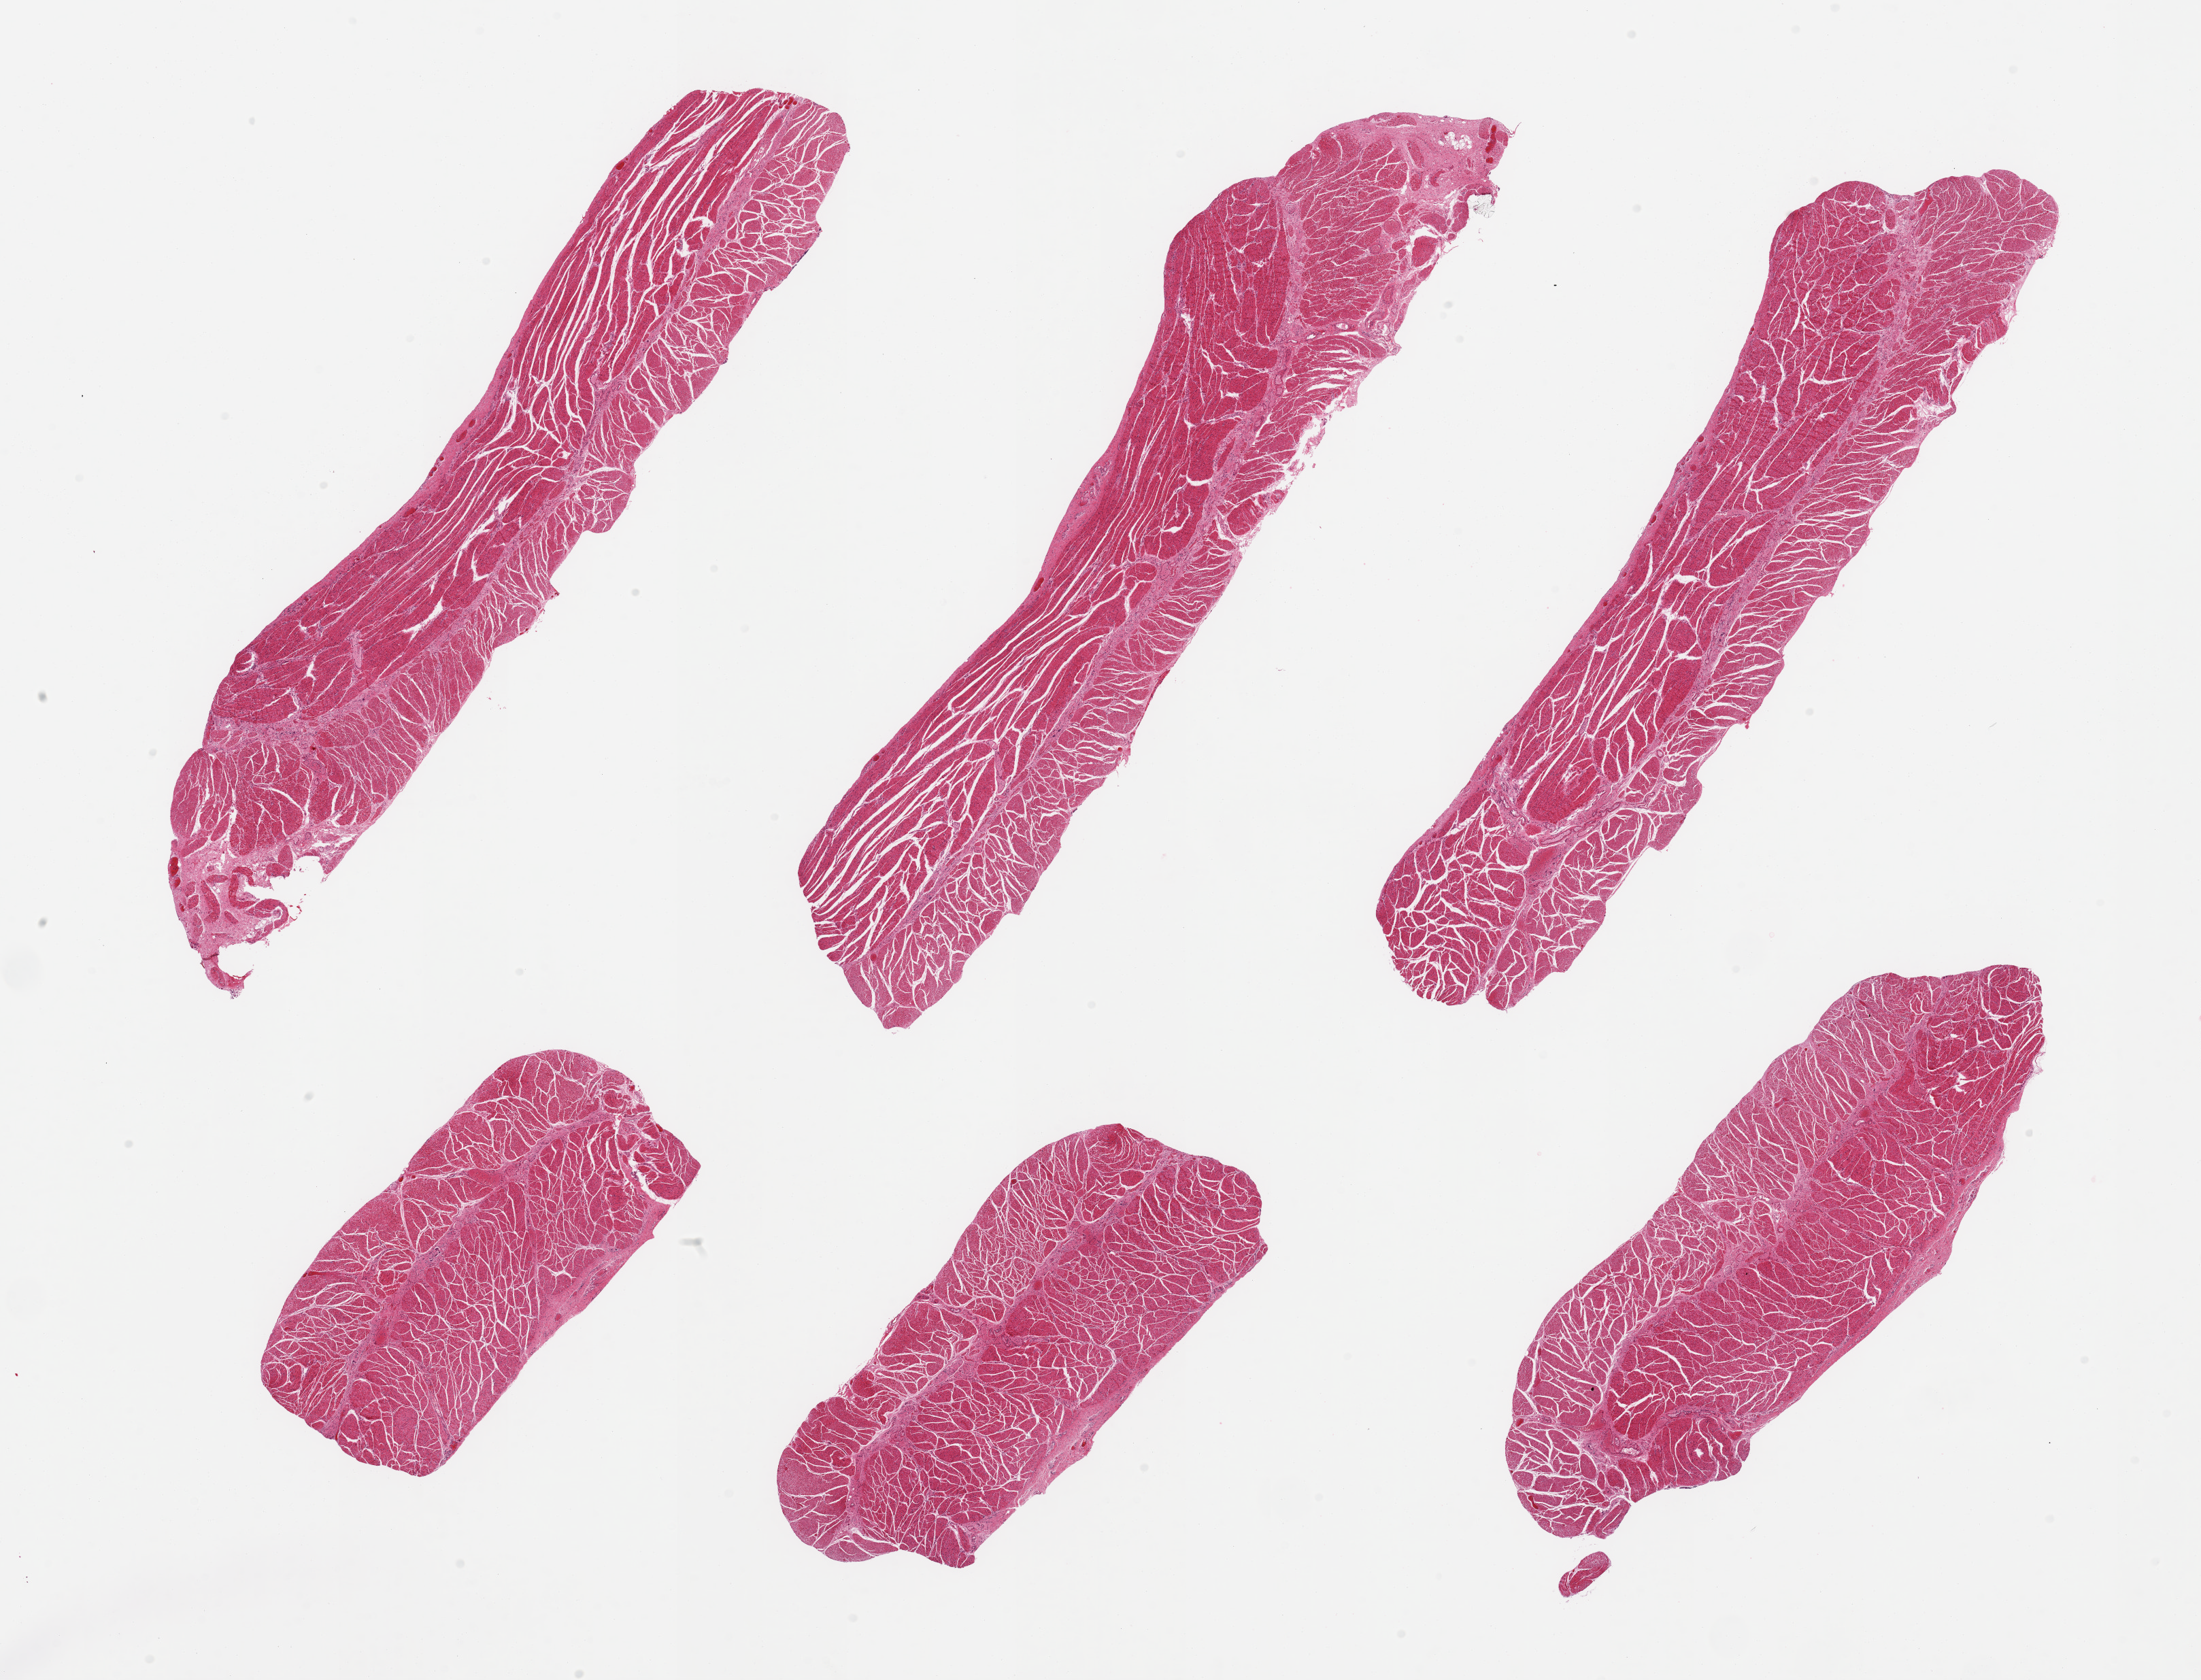
H&E whole-slide image, whole scanned area (about 25.6 x 19.5 mm, slide scanned at 20x) shown as a low-resolution overview, PAXgene-fixed, paraffin-embedded tissue, section of esophageal muscle (target tissue), donor tissue sample.
• reviewer comment on this tissue sample: 6 pieces, confirmed target muscularis